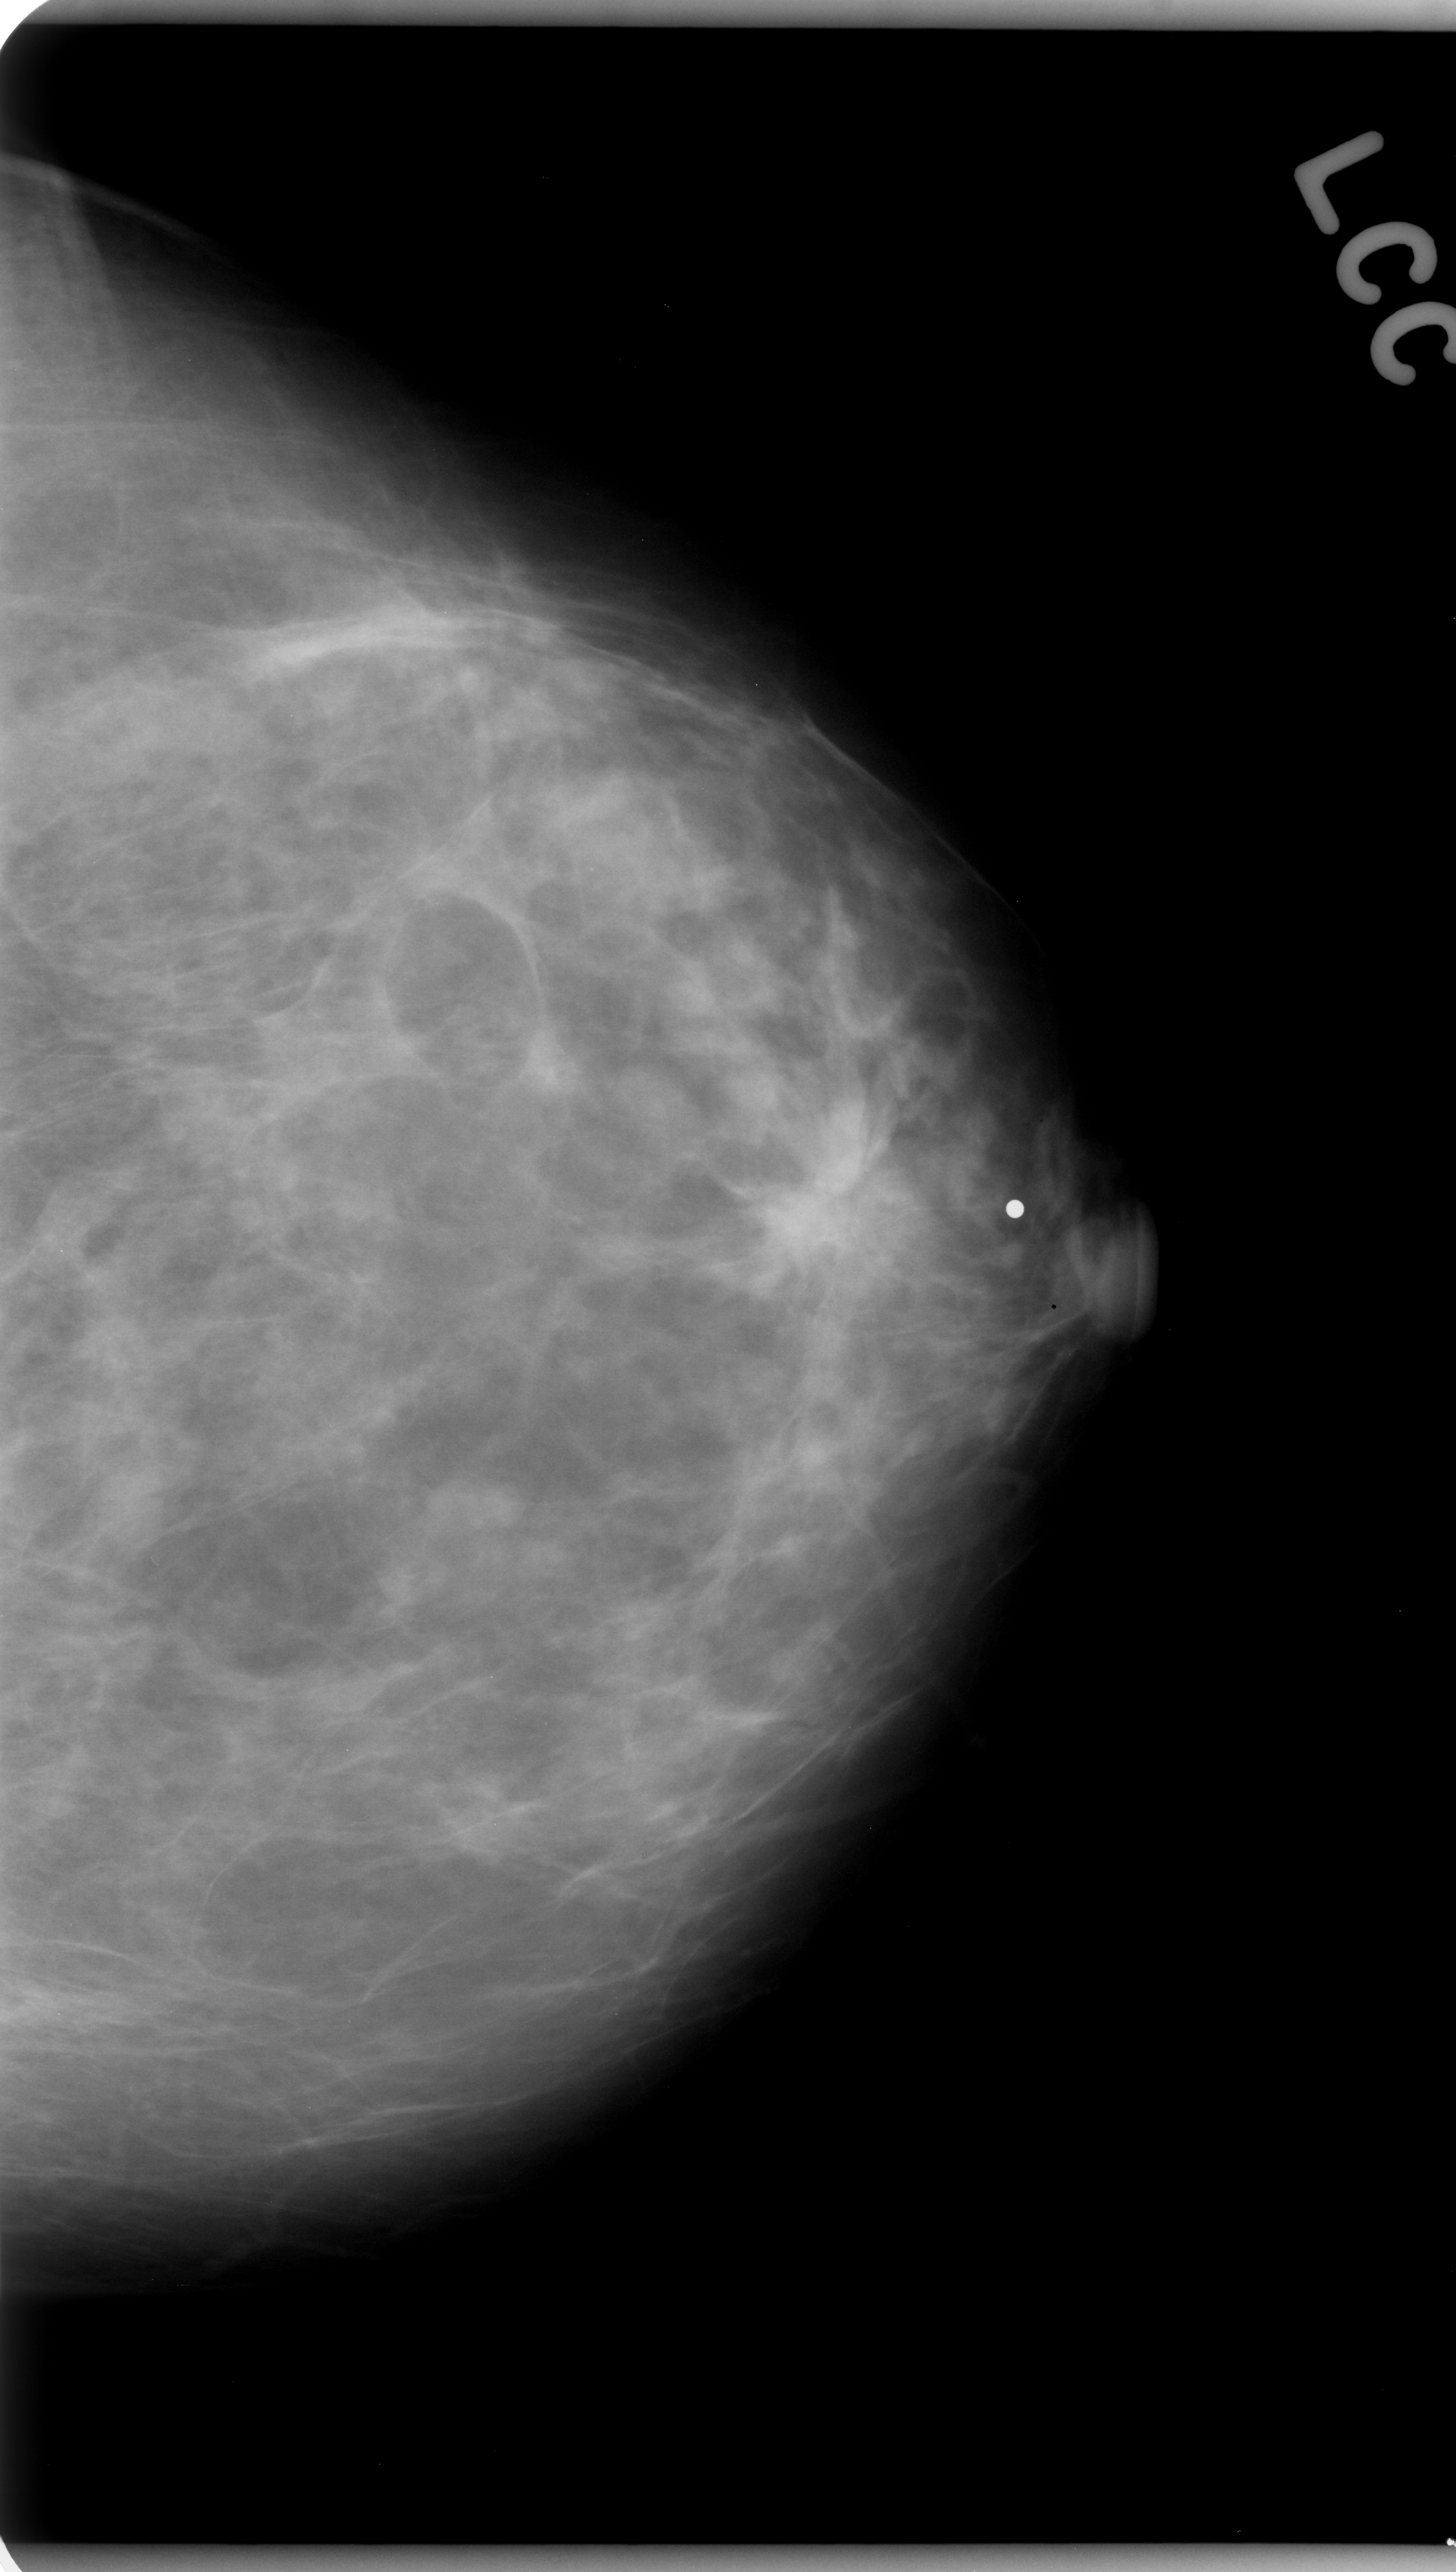
Mammogram (digitized film); left breast; CC view; BI-RADS breast density category 2 (scale 1–4); 1456 × 2572 image matrix.
Marked abnormalities (boxes around the expert regions of interest):
- mass, shape irregular, margins spiculated; BI-RADS assessment category 5; subtlety rating 5 on a 1 (subtle) to 5 (obvious) scale; pathology (as recorded): malignant: box from (x=669, y=1047) to (x=893, y=1289) px